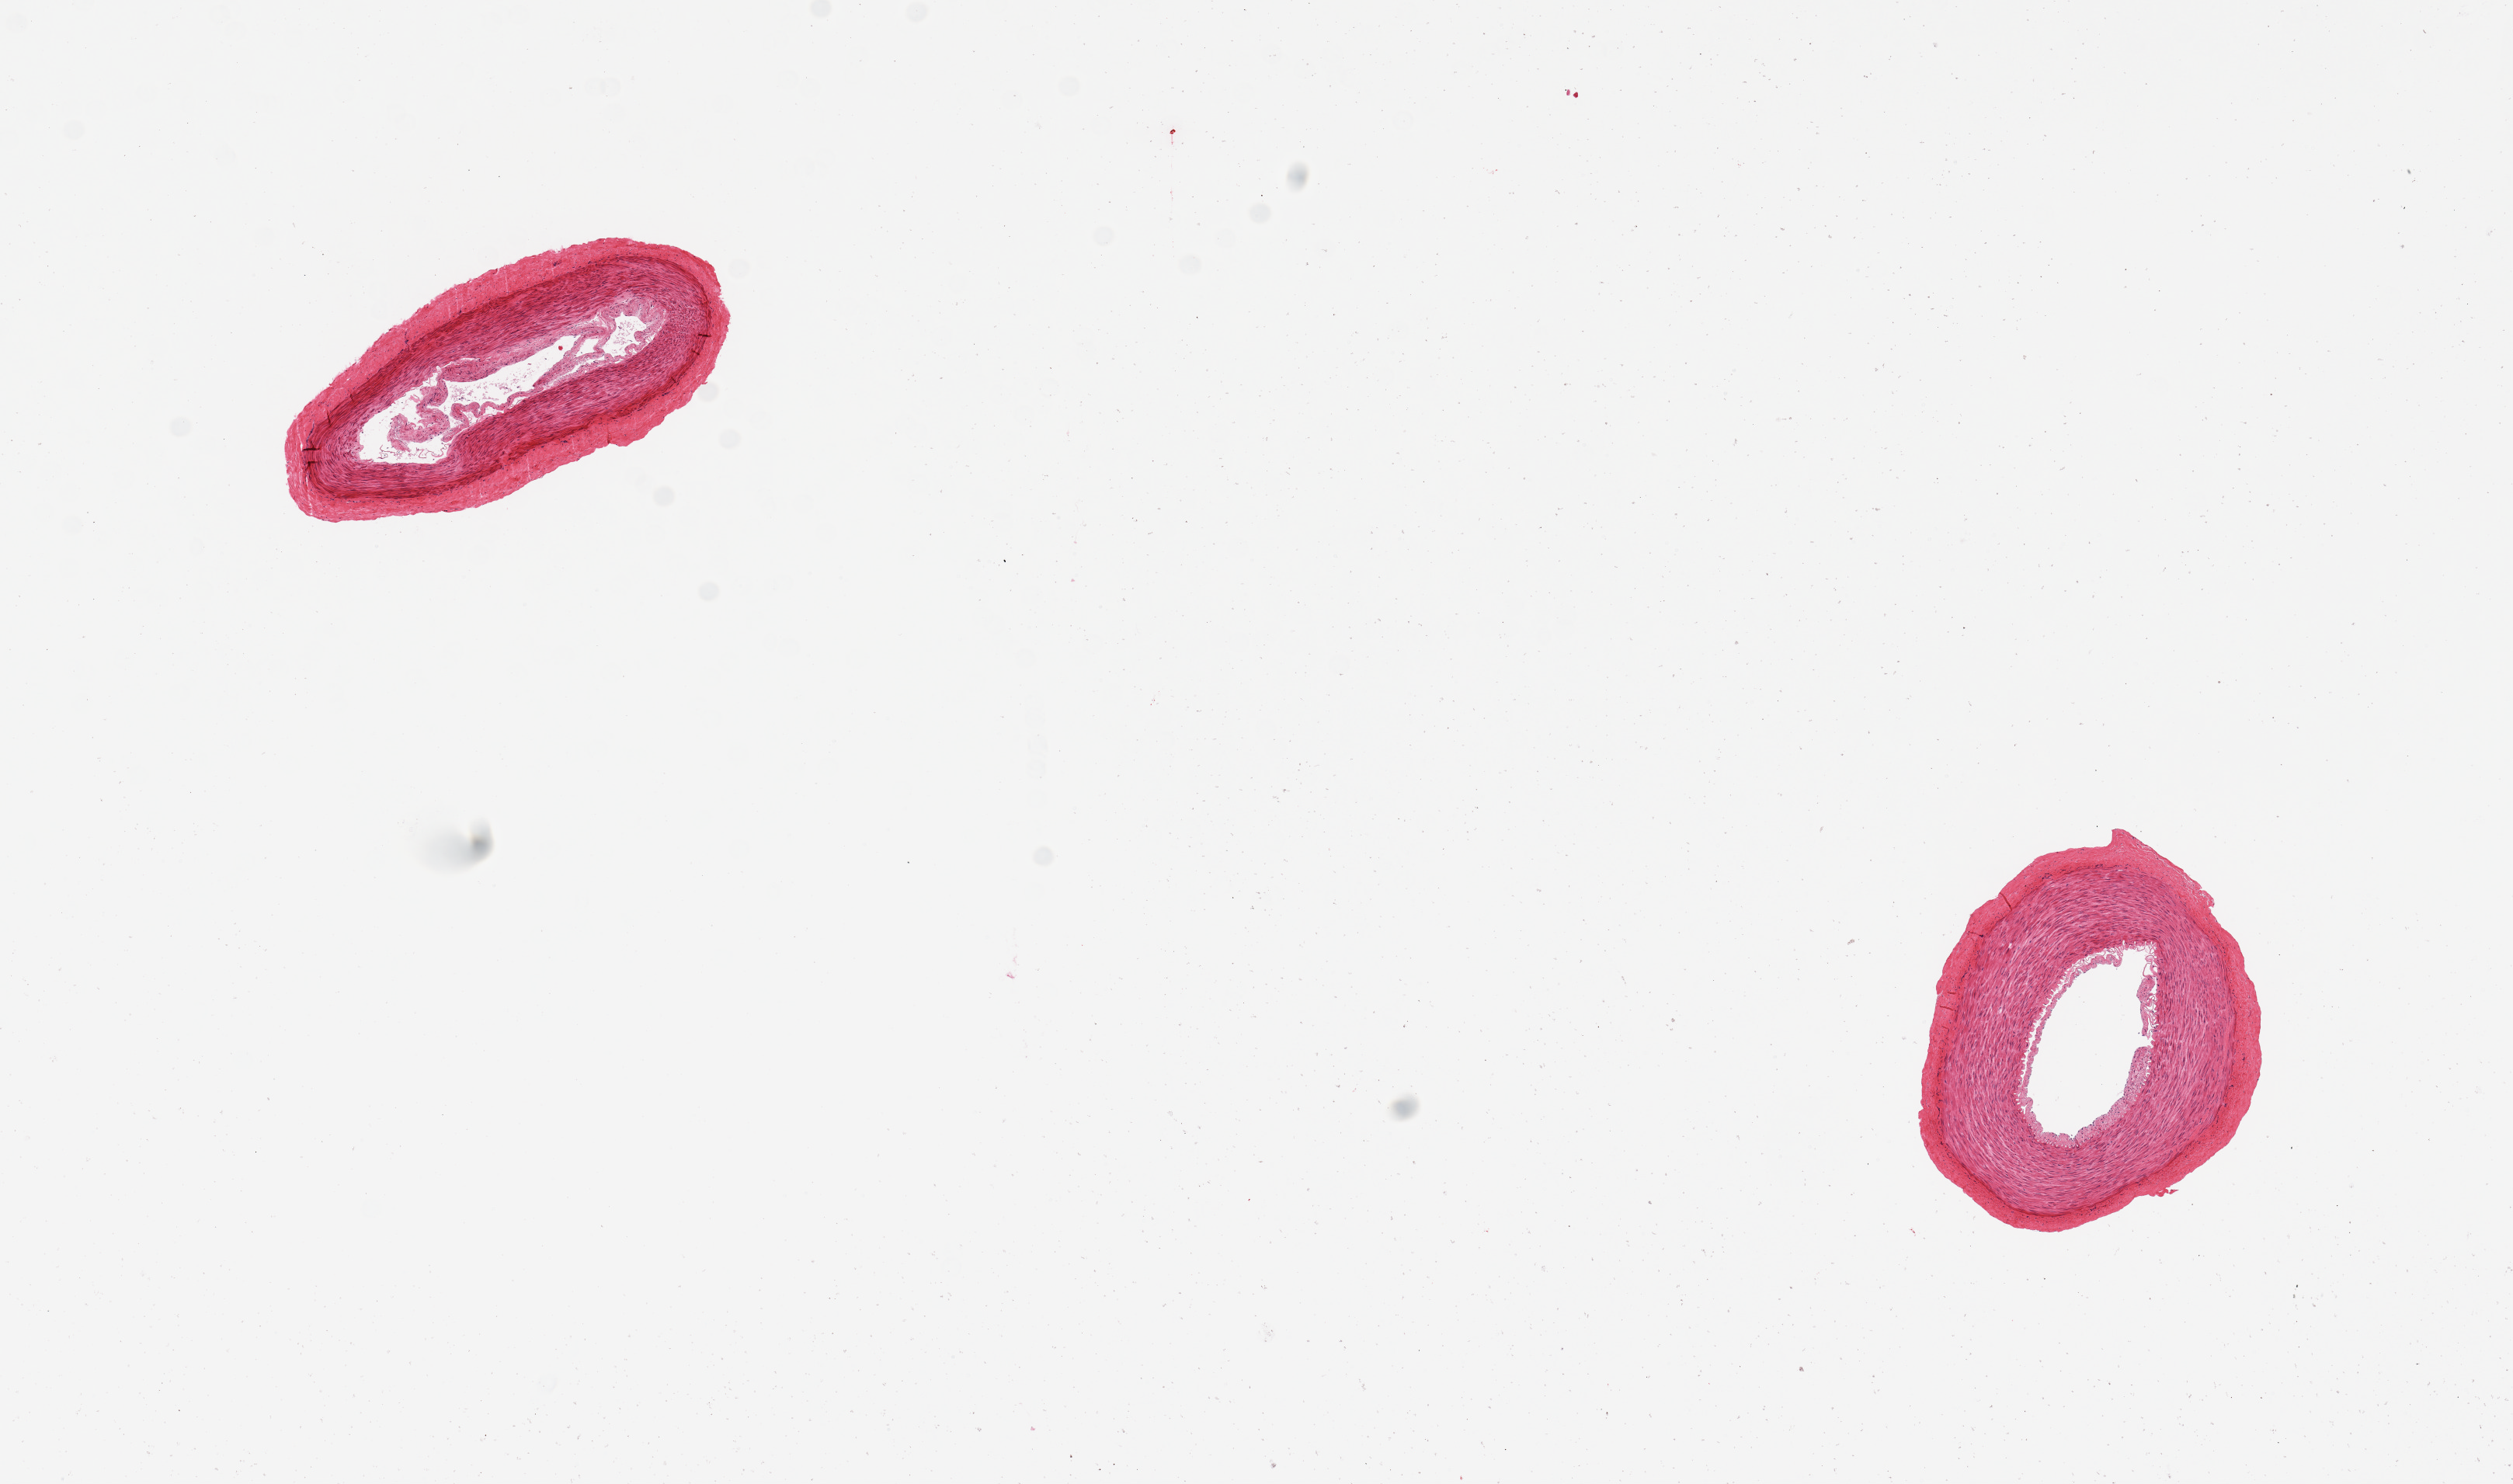
Digitized H&E-stained section — a low-resolution overview of the entire scanned area, about 12.8 x 7.6 mm; PAXgene-fixed, paraffin-embedded tissue; target tissue: tibial artery; tissue donor sample. Donor sex: male.
- pathologist's review note for this sample: 2 pieces, well trimmed